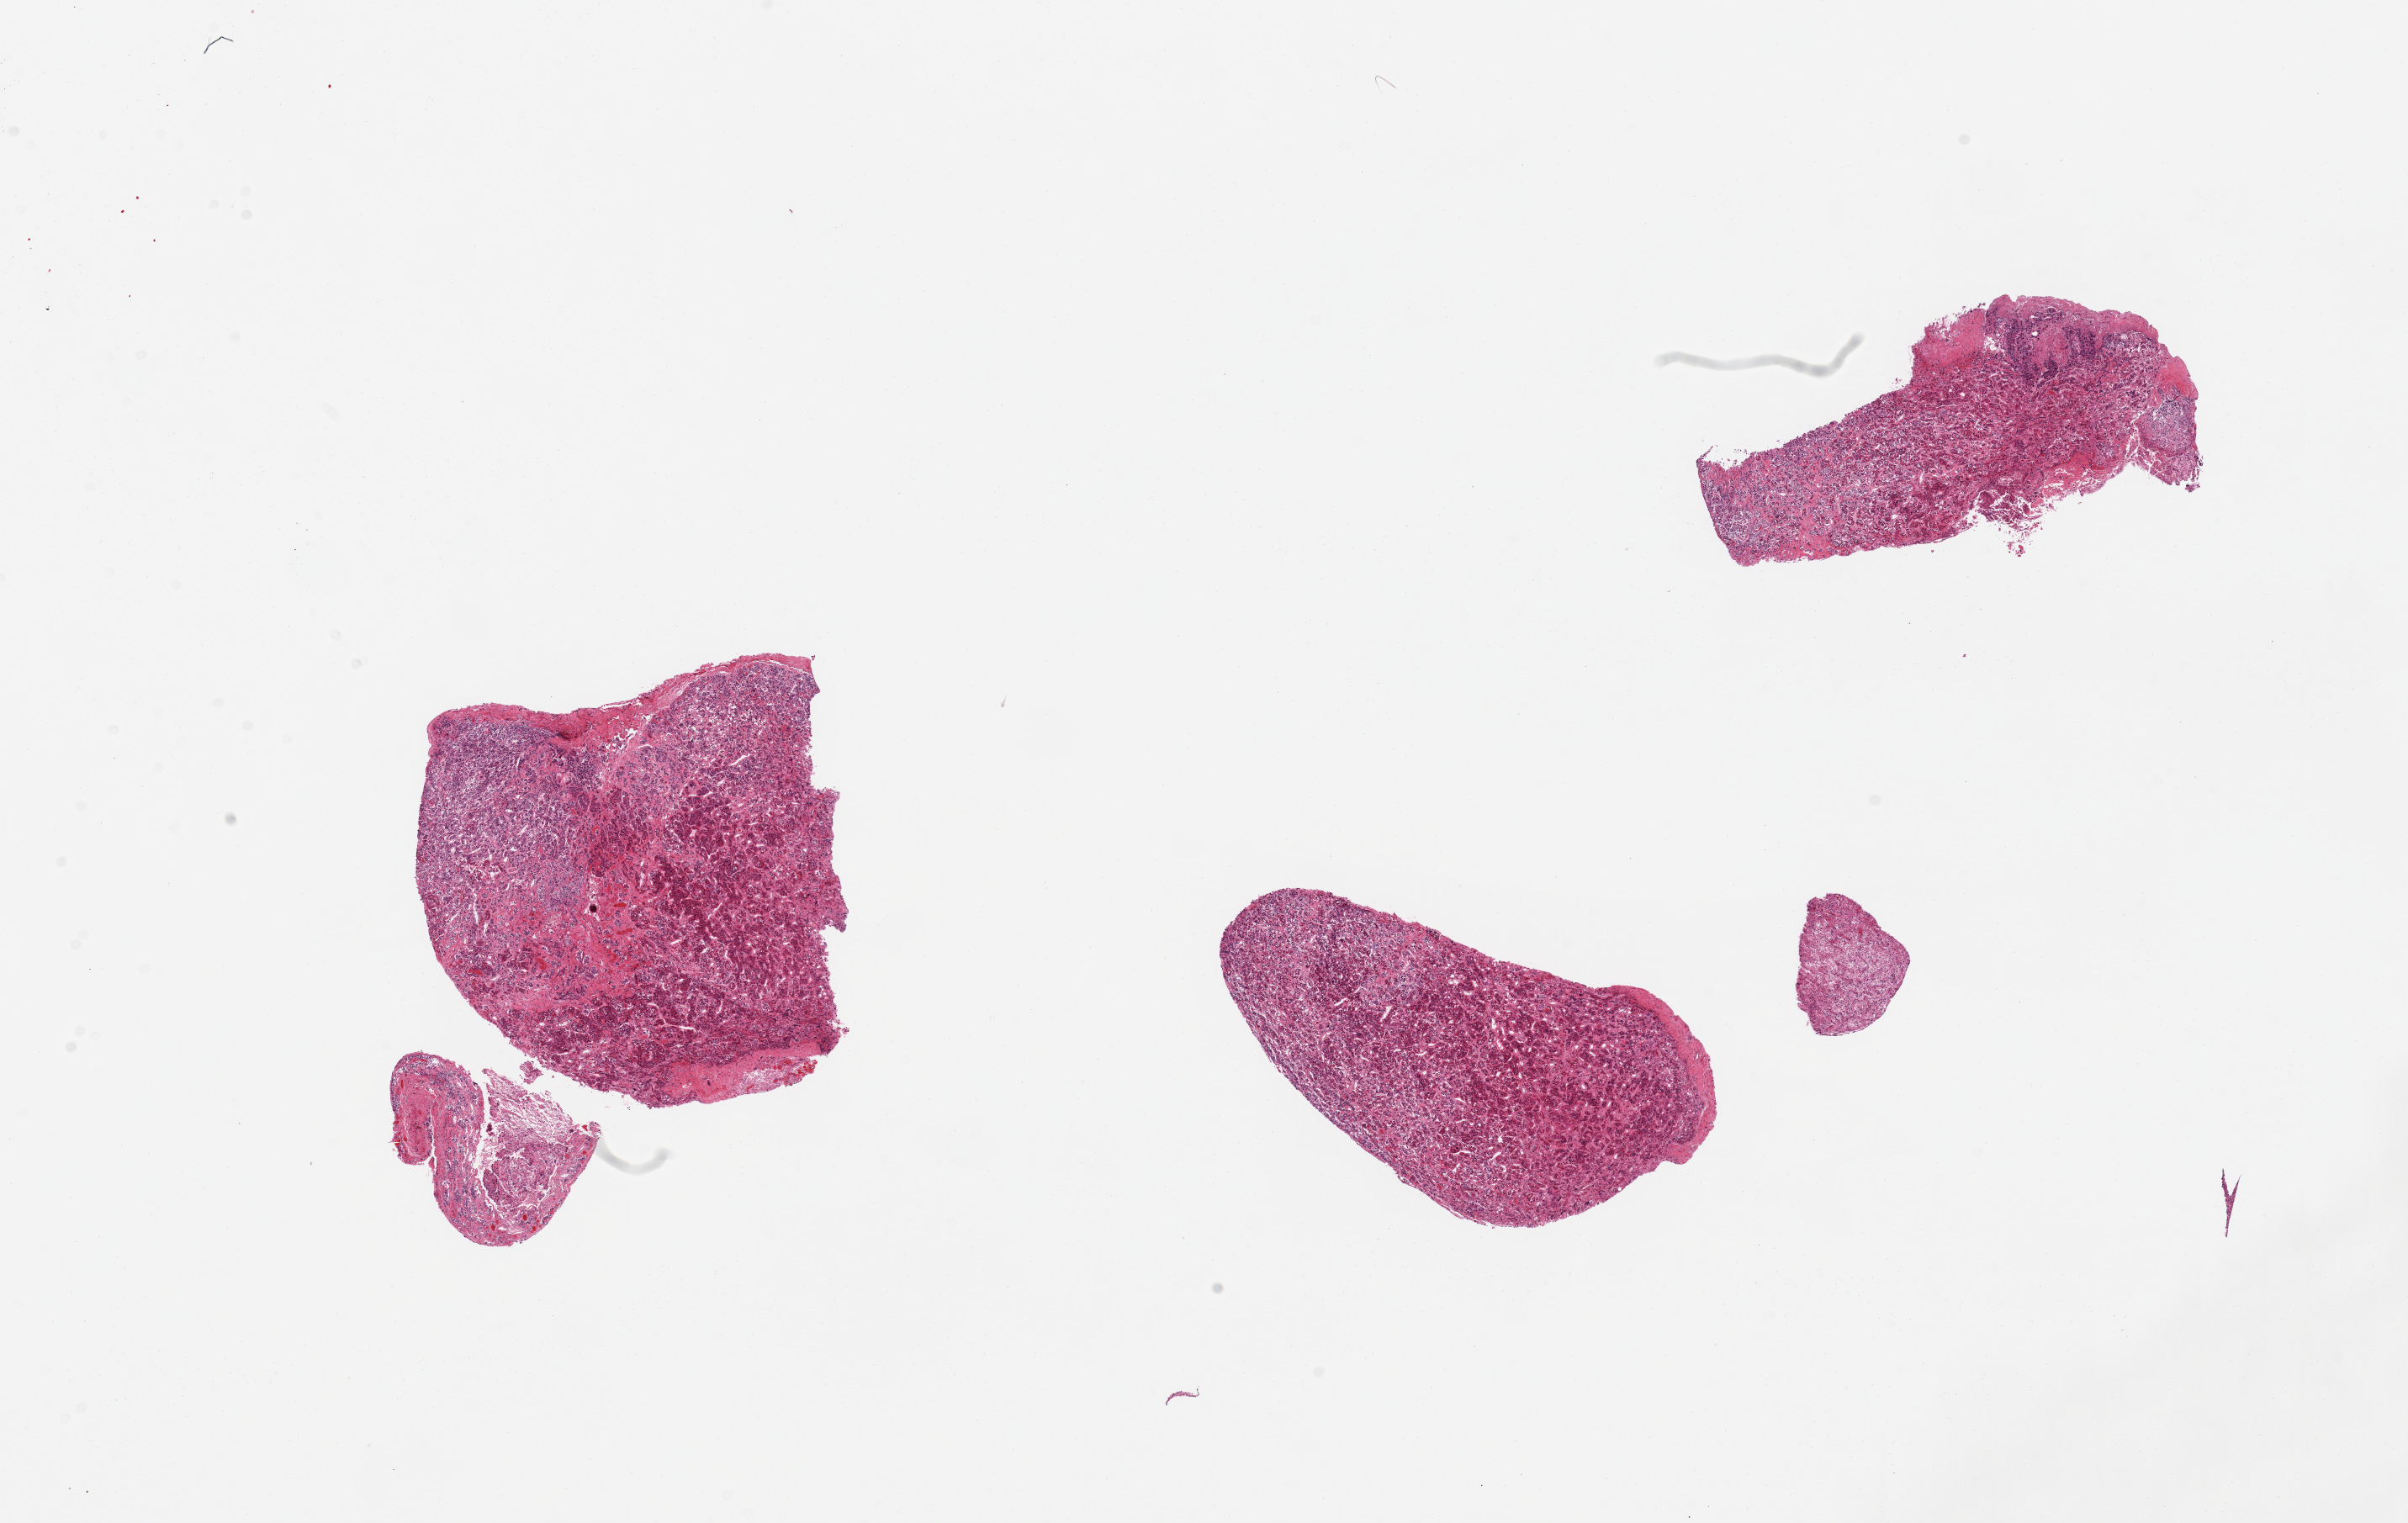
Whole-slide image, H&E stain — low-resolution overview of the scanned area, about 22.6 x 14.3 mm; PAXgene-fixed, paraffin-embedded tissue; target tissue: pituitary; tissue donor sample. Donor sex: male.
Reviewer comment on this tissue sample: 5 pieces, adenohypophysis (larger pieces) and neurohypophysis (smallest piece, marked).